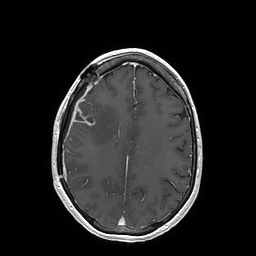
Brain MRI from a brain-tumour surgery series, one axial slice. Position 63 of 202 along the scan axis. T1-weighted post-contrast. 1 mm slice thickness. 256 × 256 image matrix, field of view 250 × 250 mm. Case-level facts recorded for this patient, not image findings: histopathology: Glioblastoma; WHO grade: 4; IDH mutation: no; tumour location: Right Insular.
Annotated regions visible in this slice (expert manual segmentation):
- tumour: box from (x=73, y=108) to (x=94, y=126) px